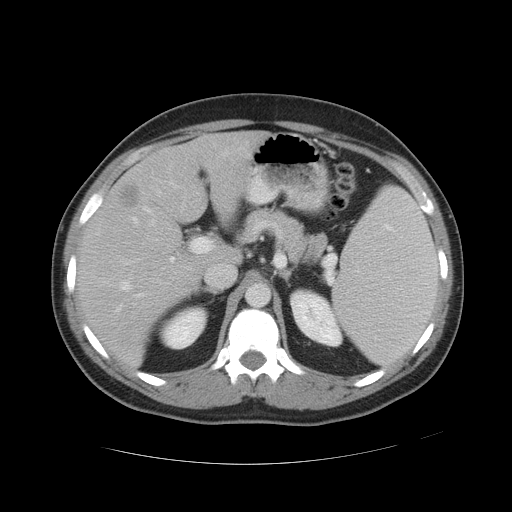
Contrast-enhanced abdominal CT, one axial slice; slice 31 of 49 in the series (ordered by position); reconstruction kernel STANDARD; 120 kVp; intravenous contrast given; soft-tissue window (W 400 / L 40 HU); 512 × 512 image matrix, field of view 422 × 422 mm. Male patient, age 42 years. Case-level facts recorded for this patient, not image findings: diagnosis: colorectal cancer liver metastases, imaged before liver resection; multiple liver metastases: yes; largest metastasis: 2.8 cm; disease in both lobes: yes.
Outlined on this slice (manually delineated by an expert):
- hepatic veins: box from (x=115, y=206) to (x=155, y=312) px
- liver: (x=78, y=134)–(x=259, y=364)
- planned liver remnant (the part of the liver to remain after resection): (x=78, y=134)–(x=259, y=364)
- portal vein (with intrahepatic branches): (x=170, y=238)–(x=213, y=274)
- liver metastasis: (x=123, y=187)–(x=139, y=208)